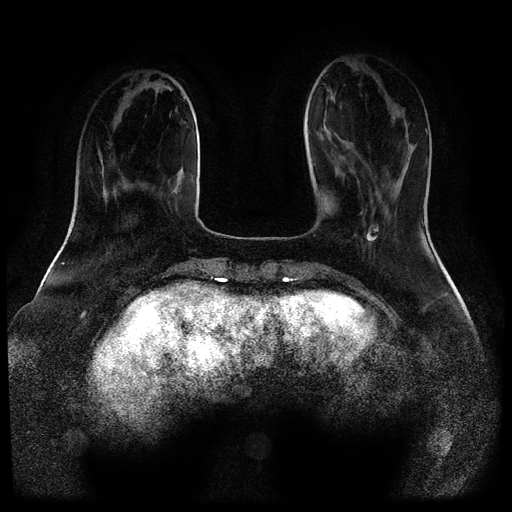
Breast MRI (dynamic contrast-enhanced, multi-phase), one axial slice. Position 29 of 116 along the scan axis. Dynamic contrast-enhanced series, time point 2 of 5 at this slice position (early post-contrast). 1.5 T. TE 2.6 ms, TR 5.3 ms. 512 × 512 image matrix, field of view 360 × 360 mm. Patient: female, 52 years.
Outlined on this slice (semi-automatic segmentation, software-assisted and operator-edited):
- breast lesion (labelled 'tumour' in the annotation; benign lesions carry a separate 'benign' label): box from (x=366, y=224) to (x=379, y=244) px